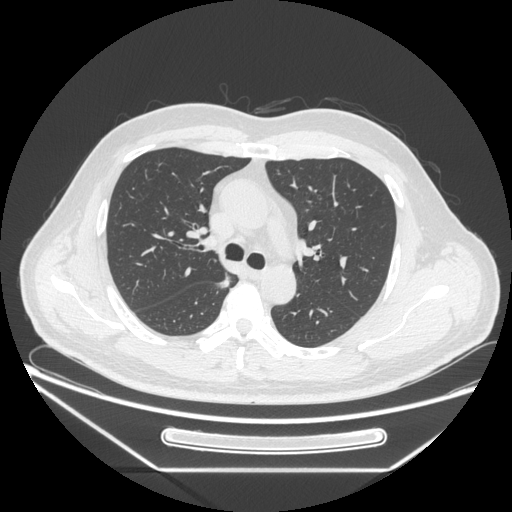
Chest CT, one axial slice; slice 167 of 271 in the series (ordered by position); 120 kVp; lung window (W 1500 / L -600 HU); 512 × 512 image matrix. Male patient, age 49 years. Case-level facts recorded for this patient, not image findings: clinical TNM (as recorded): T1b N0 M0.
Annotated regions visible in this slice (bounding box drawn by a radiologist):
- lung tumour (recorded histology: adenocarcinoma): bounding box <218,274,234,295> (left, top, right, bottom; pixels)